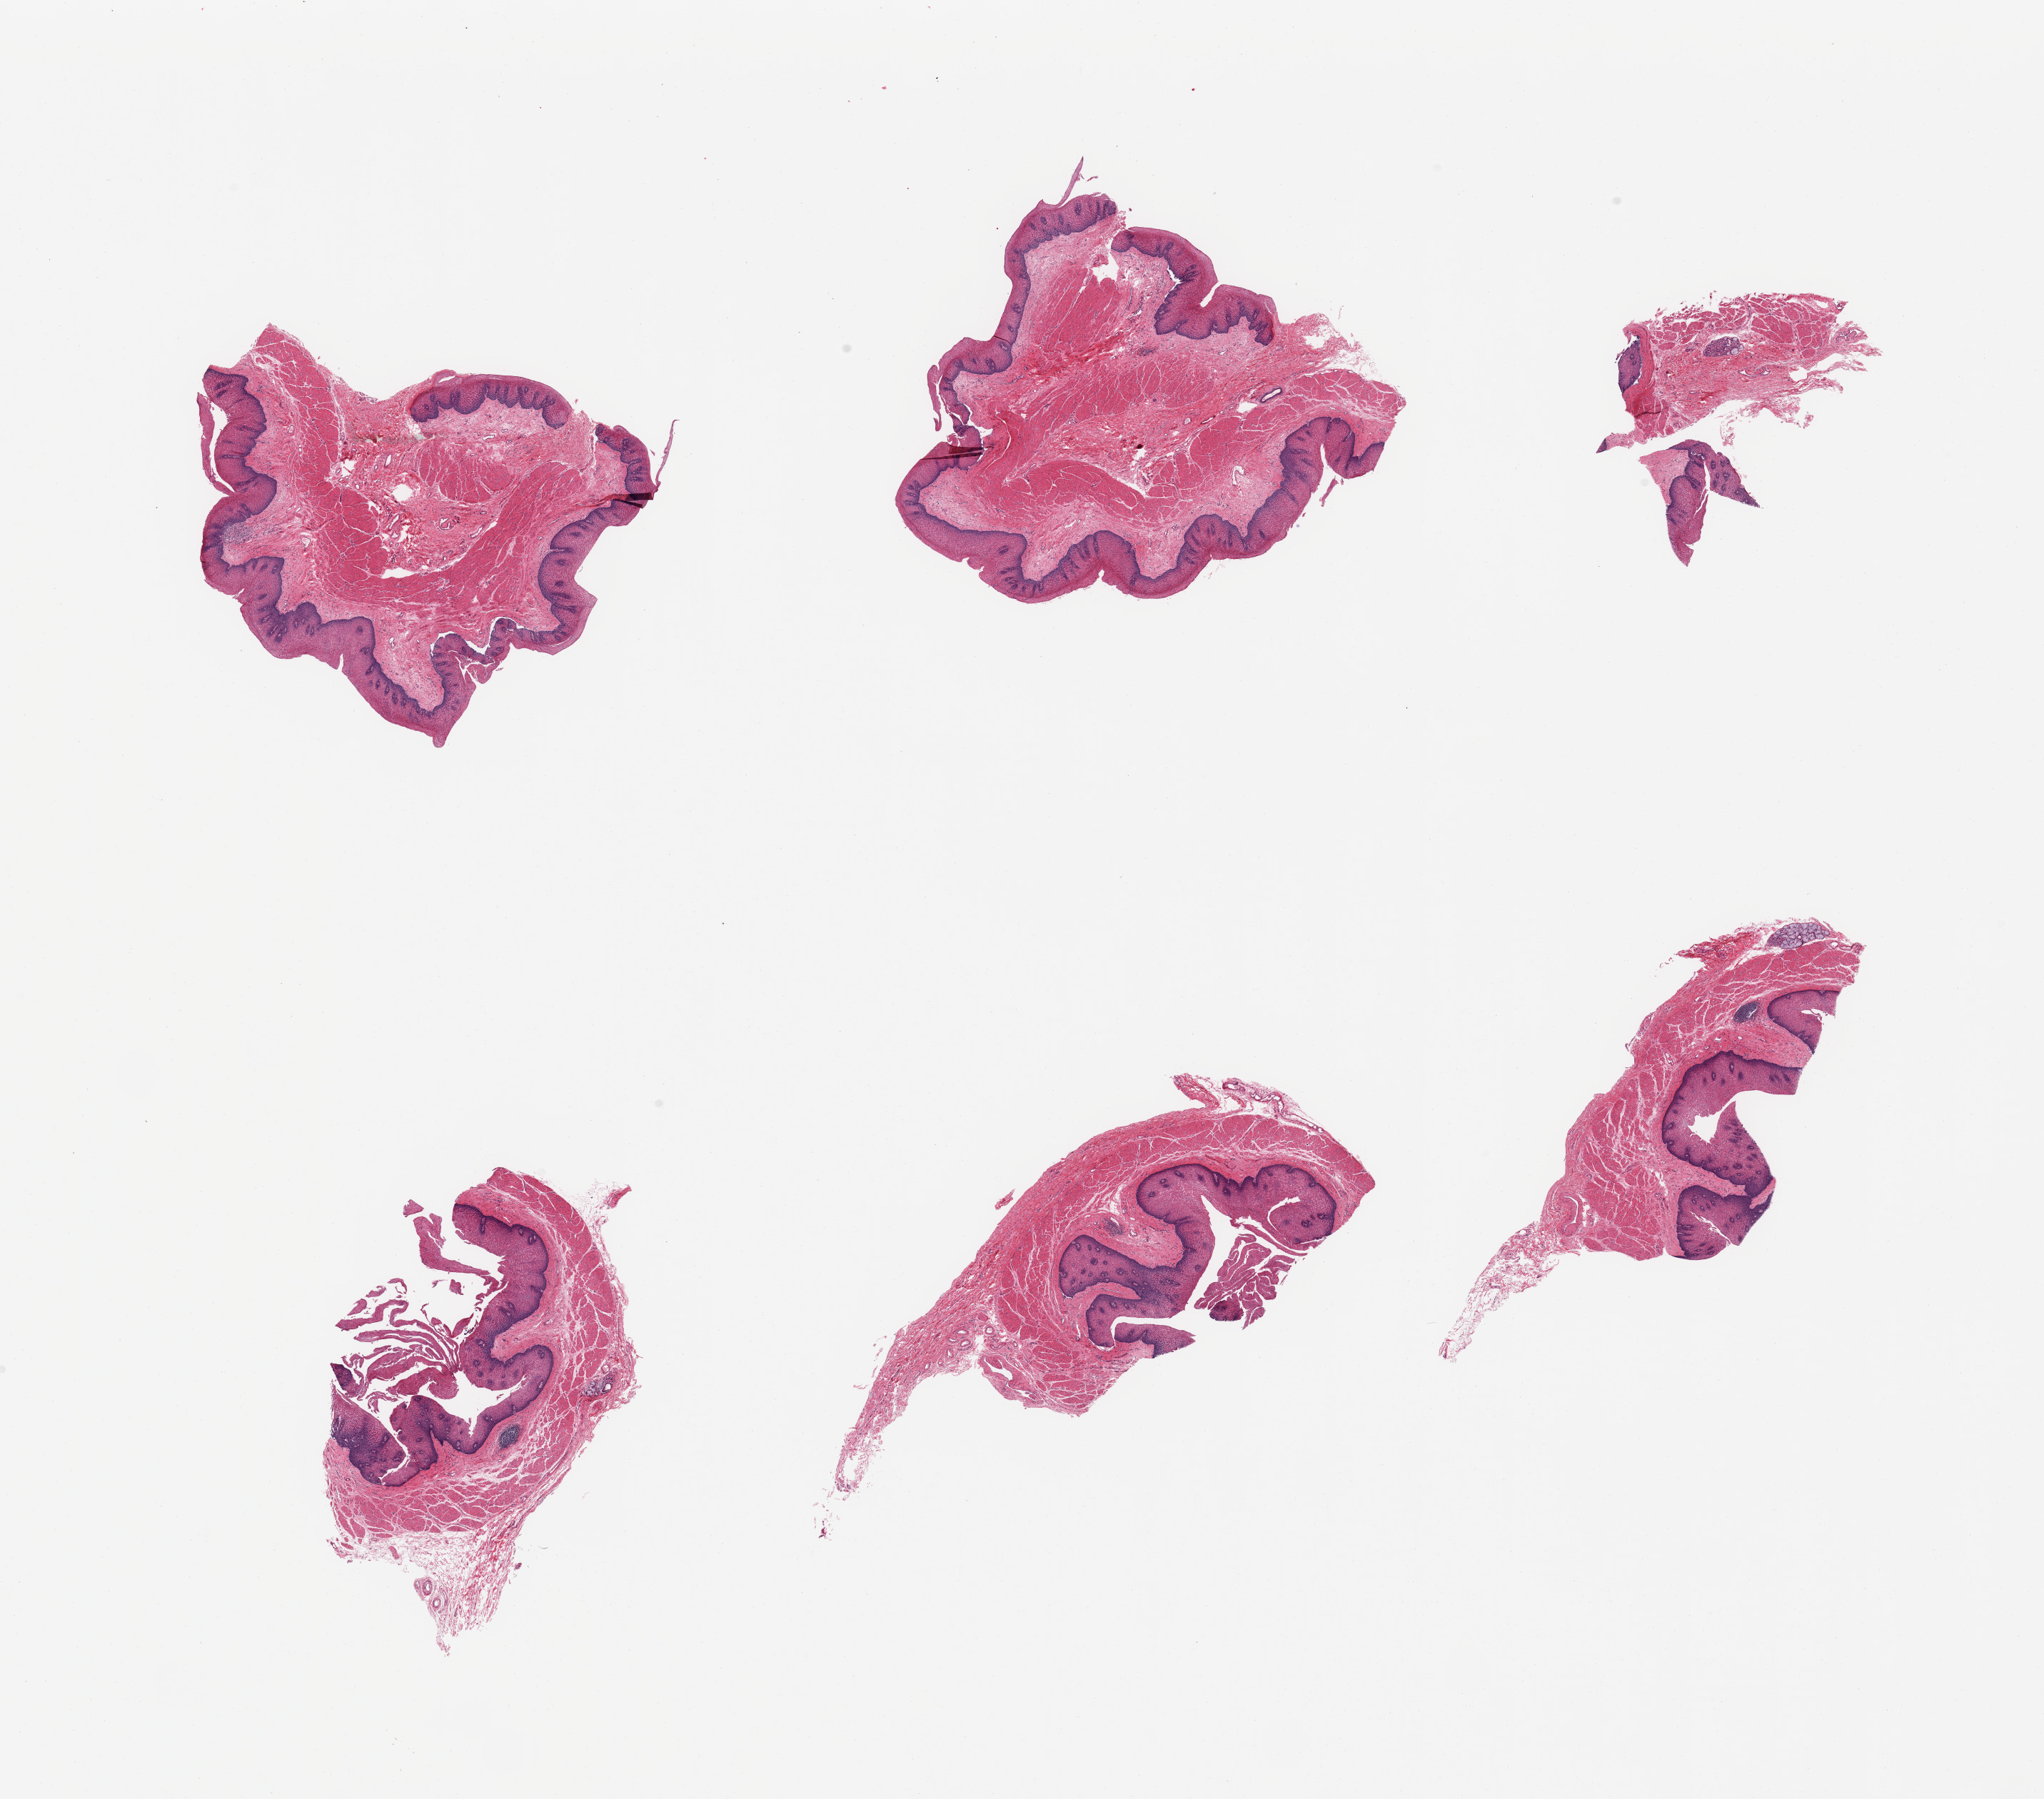
Whole-slide image, haematoxylin and eosin stain — whole scanned area (about 22.6 x 19.9 mm) shown as a low-resolution overview, PAXgene-fixed, paraffin-embedded tissue, section of esophageal mucous membrane (target tissue), tissue donor sample. Male donor.
Reviewer comment on this tissue sample: 6 pieces; squamous mucosa up to ~0.3mm, ~20-30% thickness.